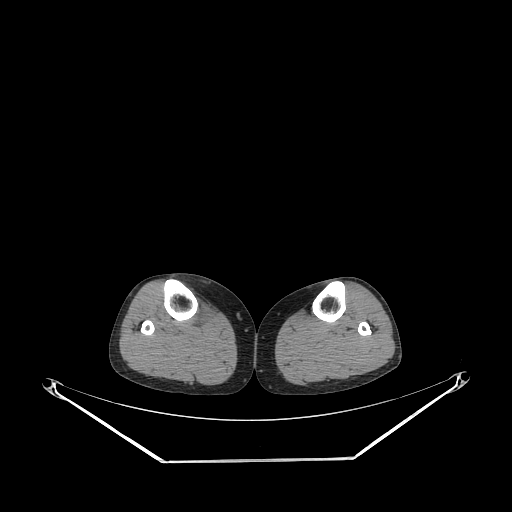
CT of an extremity soft-tissue mass (from a PET/CT study), one axial slice. Slice 150 of 267 in the series (ordered by position). 140 kVp. Soft-tissue window (W 400 / L 40 HU). 512 × 512 image matrix, field of view 500 × 500 mm. Female patient. From the clinical record (not read from this slice): histological type: undifferentiated – high grade; grade: high; site of the primary tumour: right thigh.
Outlined on this slice (expert contour drawn on MRI and transferred to this co-registered scan by the dataset authors):
- gross tumour volume (mass): bounding box <192,301,216,328> (left, top, right, bottom; pixels)